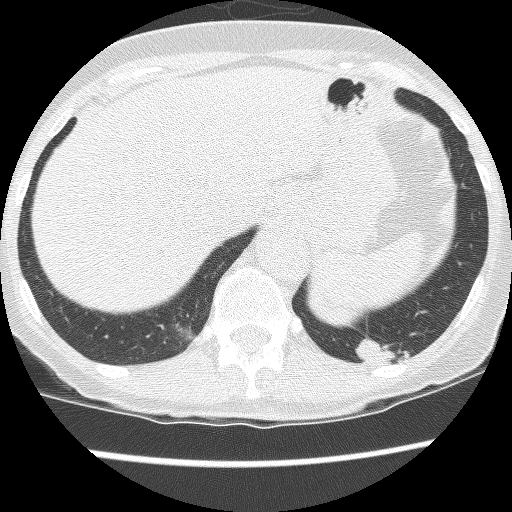
Low-dose screening chest CT, axial slice. Third annual screen. Lung window (W 1500 / L -600 HU). 2.5 mm slice thickness. Lung (sharp) reconstruction kernel (BONE). Slice 107 of 130 in the series. 512 × 512 image matrix. Female participant, aged 61 years at enrolment.
Expert-annotated lung lesion, box from (x=337, y=296) to (x=439, y=385) px. The screening reader recorded 2 non-calcified nodules or masses ≥4 mm on this exam (left lower lobe, left lower lobe); which of them this box marks is not recorded. Later outcome: lung cancer diagnosed 166 days after this screen — non-small cell carcinoma, left lower lobe, poorly differentiated (G3), stage IB (AJCC 6th edition), 100 mm at pathology.